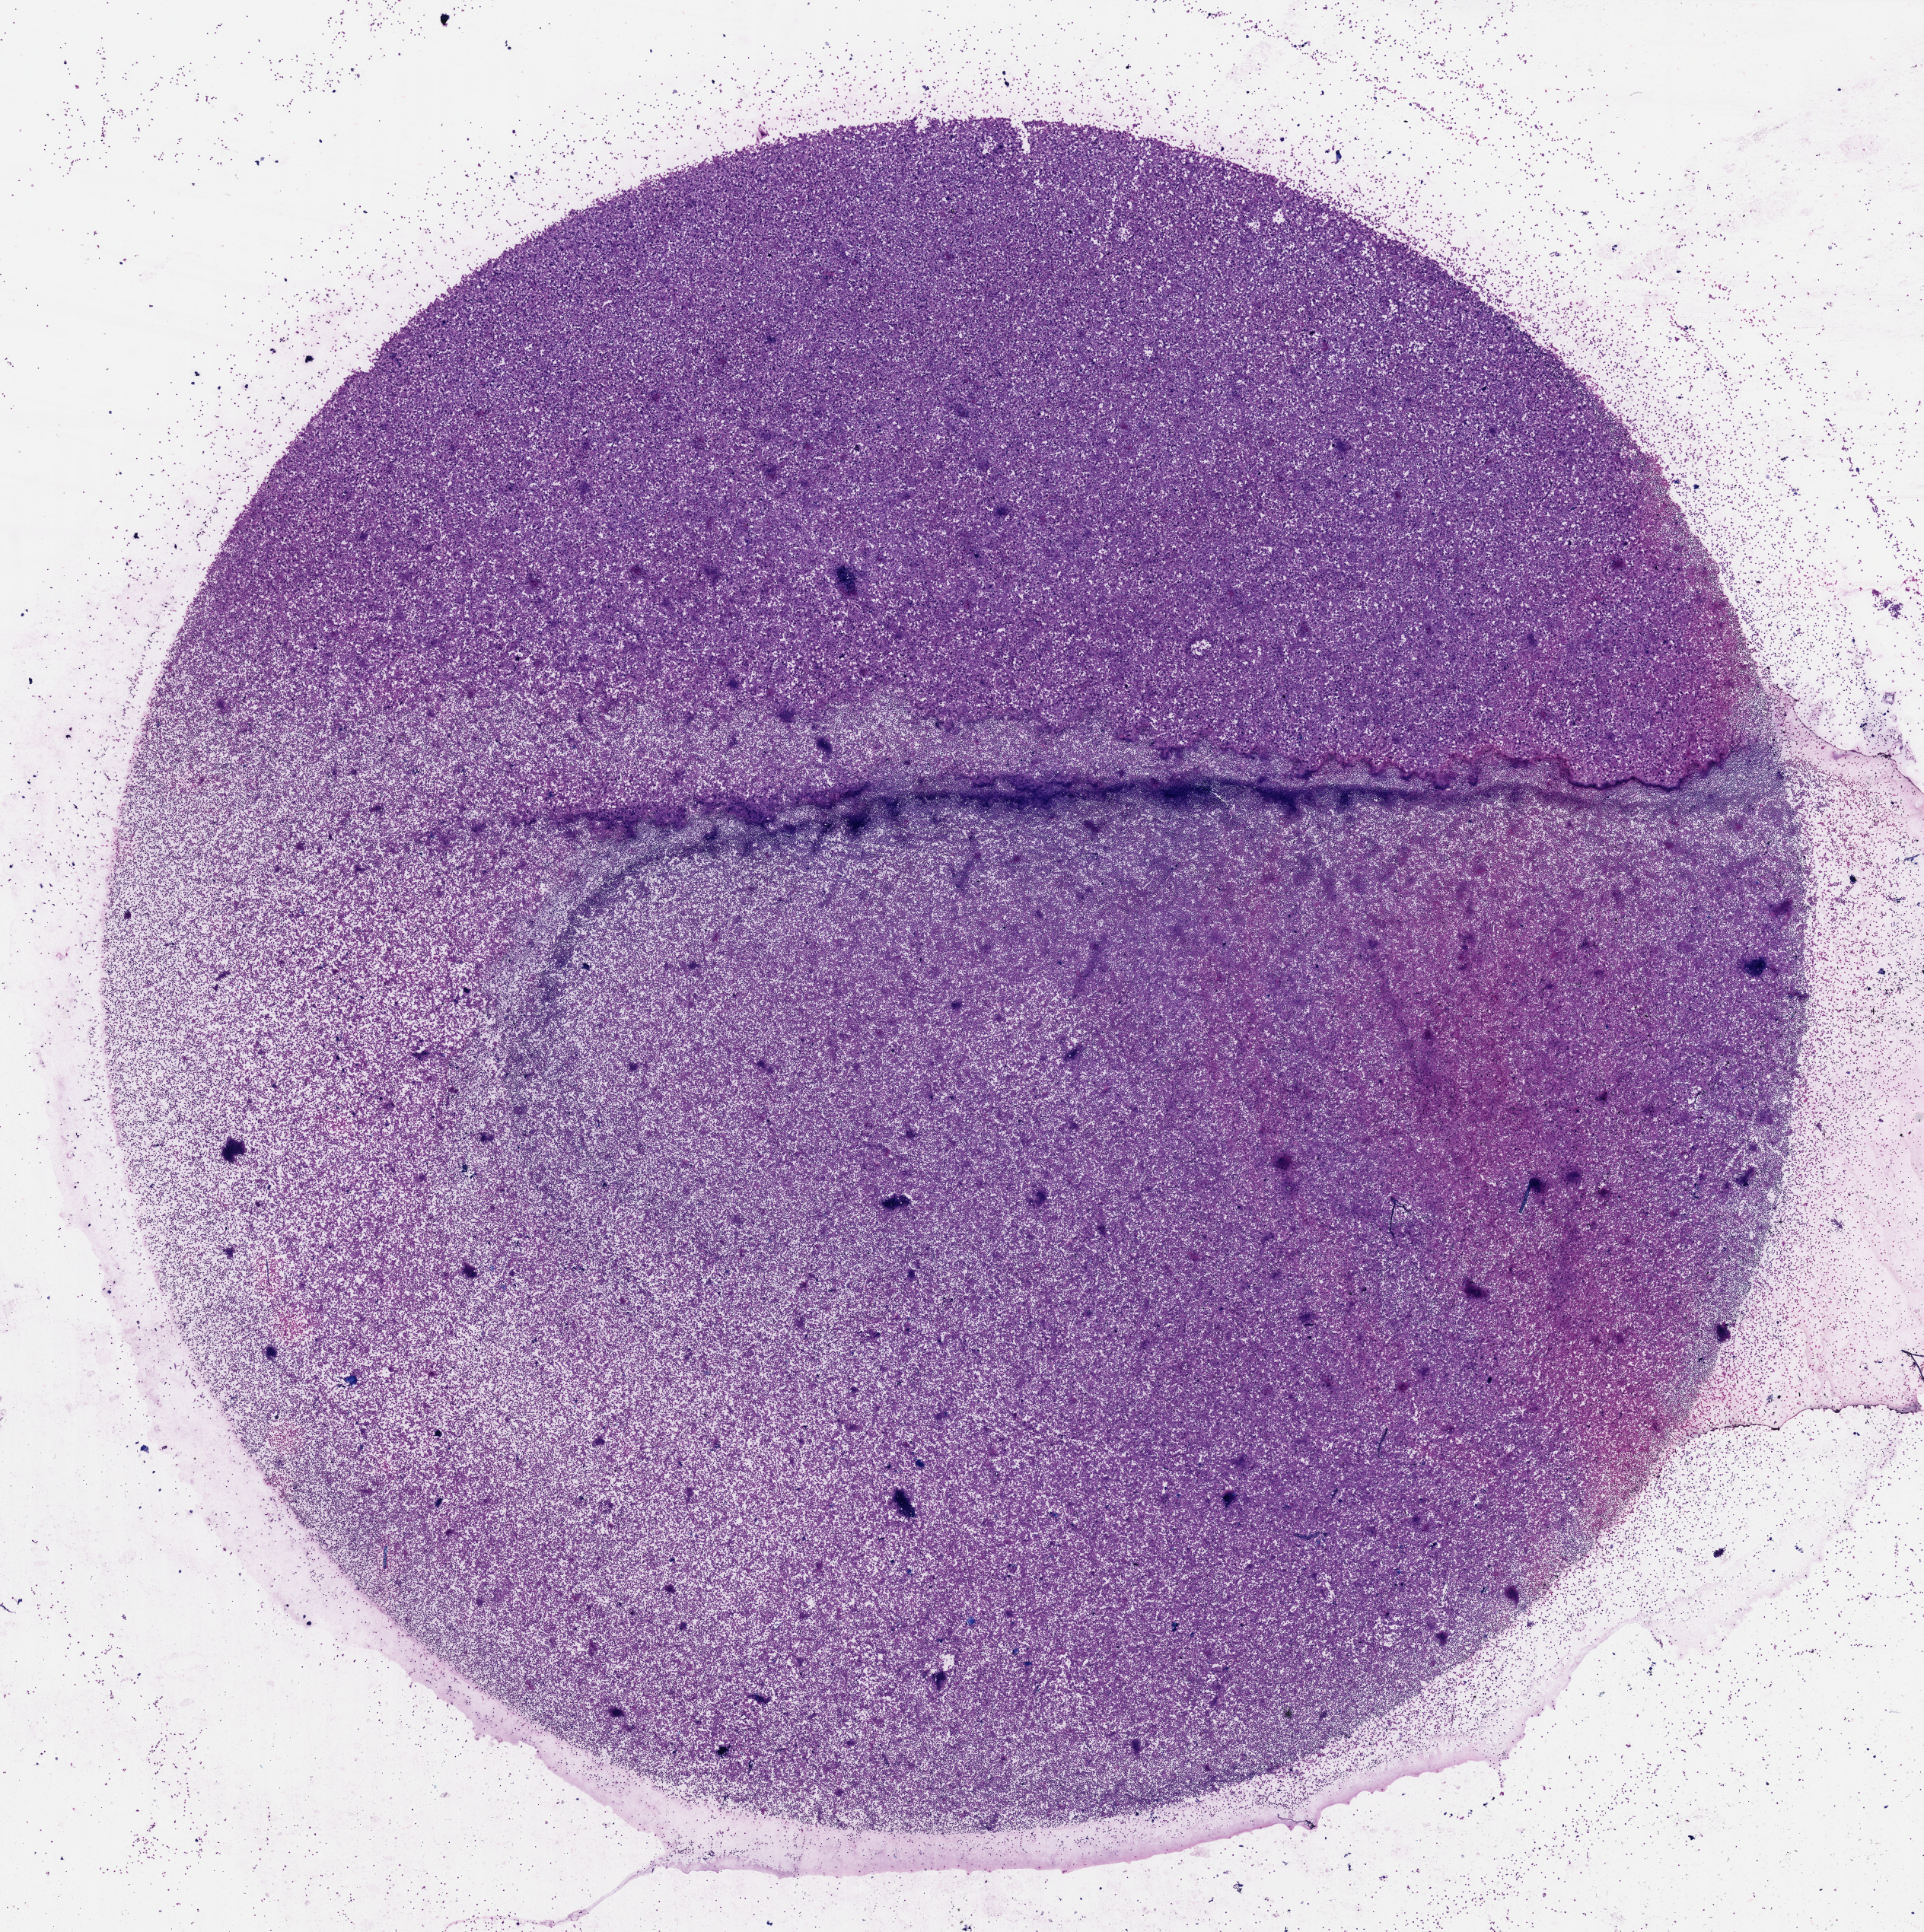
Digitized H&E-stained tissue section (whole slide) — shown as a low-resolution overview of the whole scanned area (about 20.0 x 20.0 mm), bone marrow (leukaemic) sample. Female, 46 y/o. Blasts: 85%.
WHO classification: AML with minimal differentiation. FAB classification: M0. Diagnosis: Acute Myeloid Leukemia.